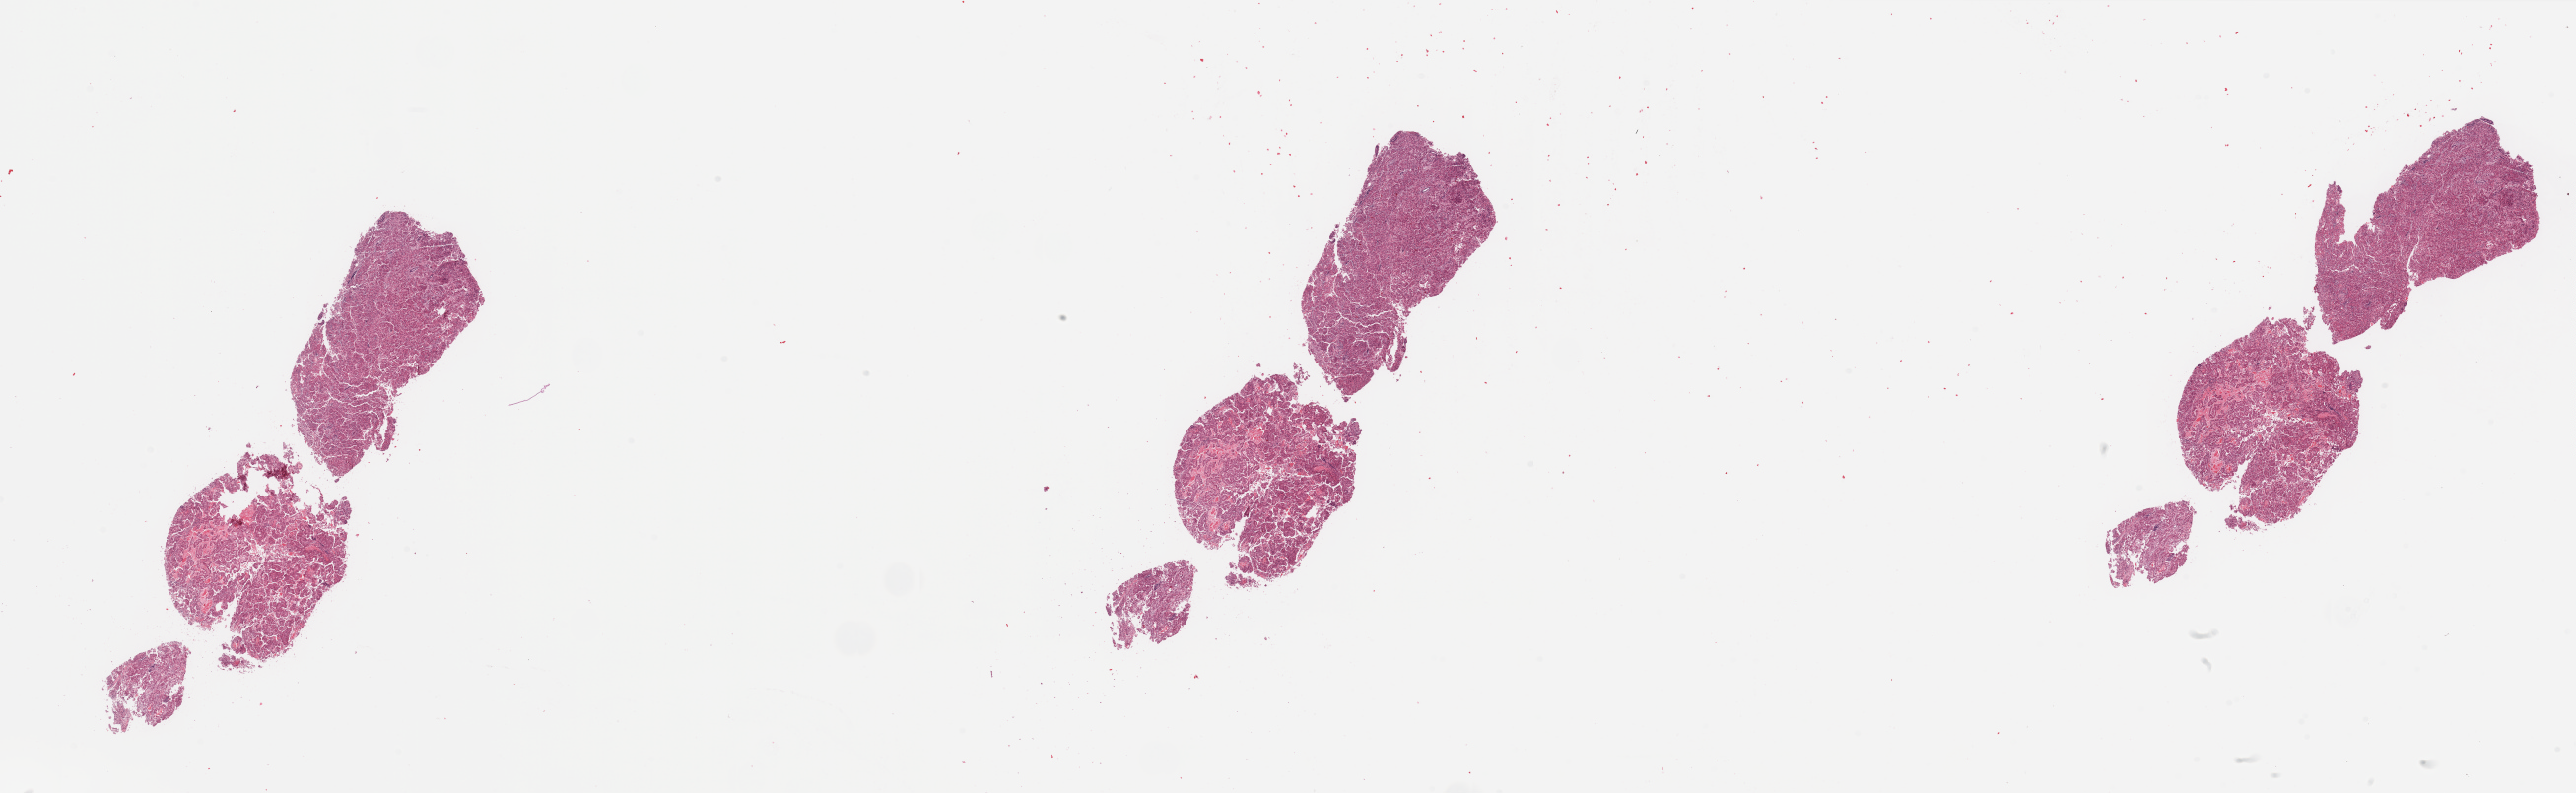
Digitized H&E tissue section (whole slide) — low-resolution overview of the scanned area, about 41.3 x 12.7 mm (slide scanned at 20x). Tumour tissue sample, uterus. Female, 72 y/o. Histologic grade: G3 (poorly differentiated).
Histologic diagnosis: Endometrioid adenocarcinoma, NOS. AJCC pathologic stage: III.